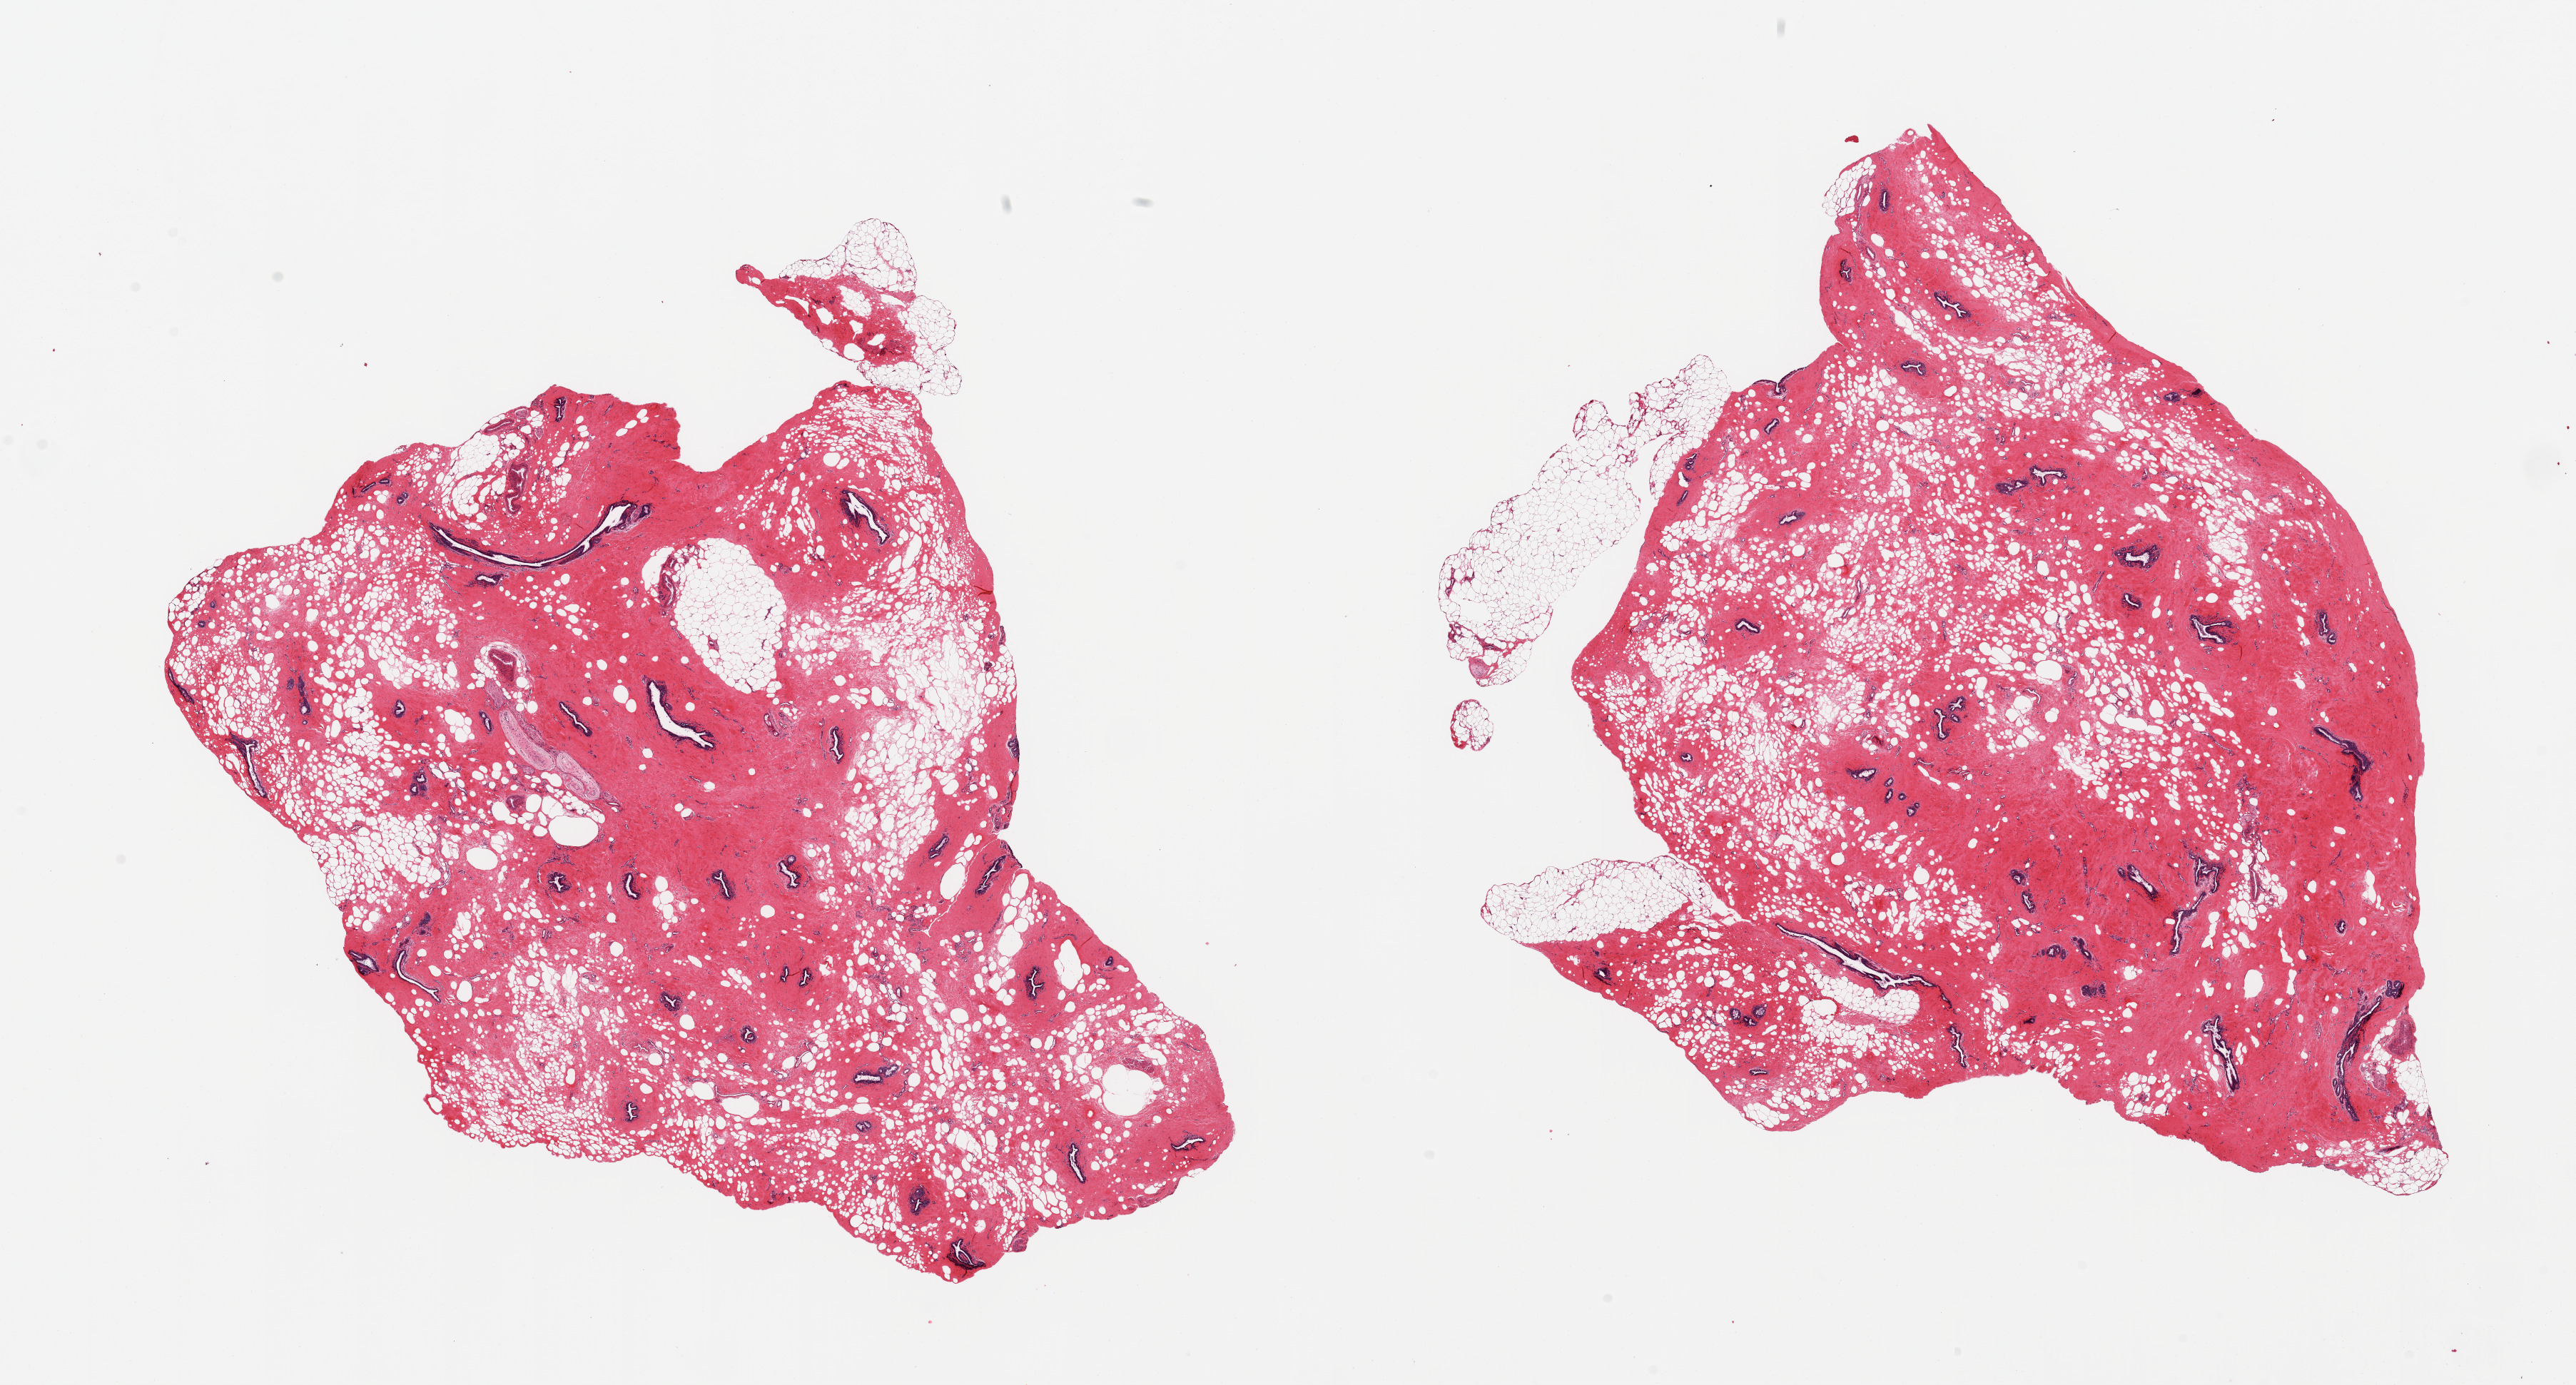
Haematoxylin and eosin whole-slide image — a low-resolution overview of the entire scanned area, about 28.5 x 15.3 mm, PAXgene-fixed, paraffin-embedded tissue, sampled site (target tissue): breast, donor tissue sample. Donor sex: male.
Reviewer comment on this tissue sample: 2 pieces, gynecomastoid ductal and stromal hyperplasia; Numerous ductal elements present, good specimen.